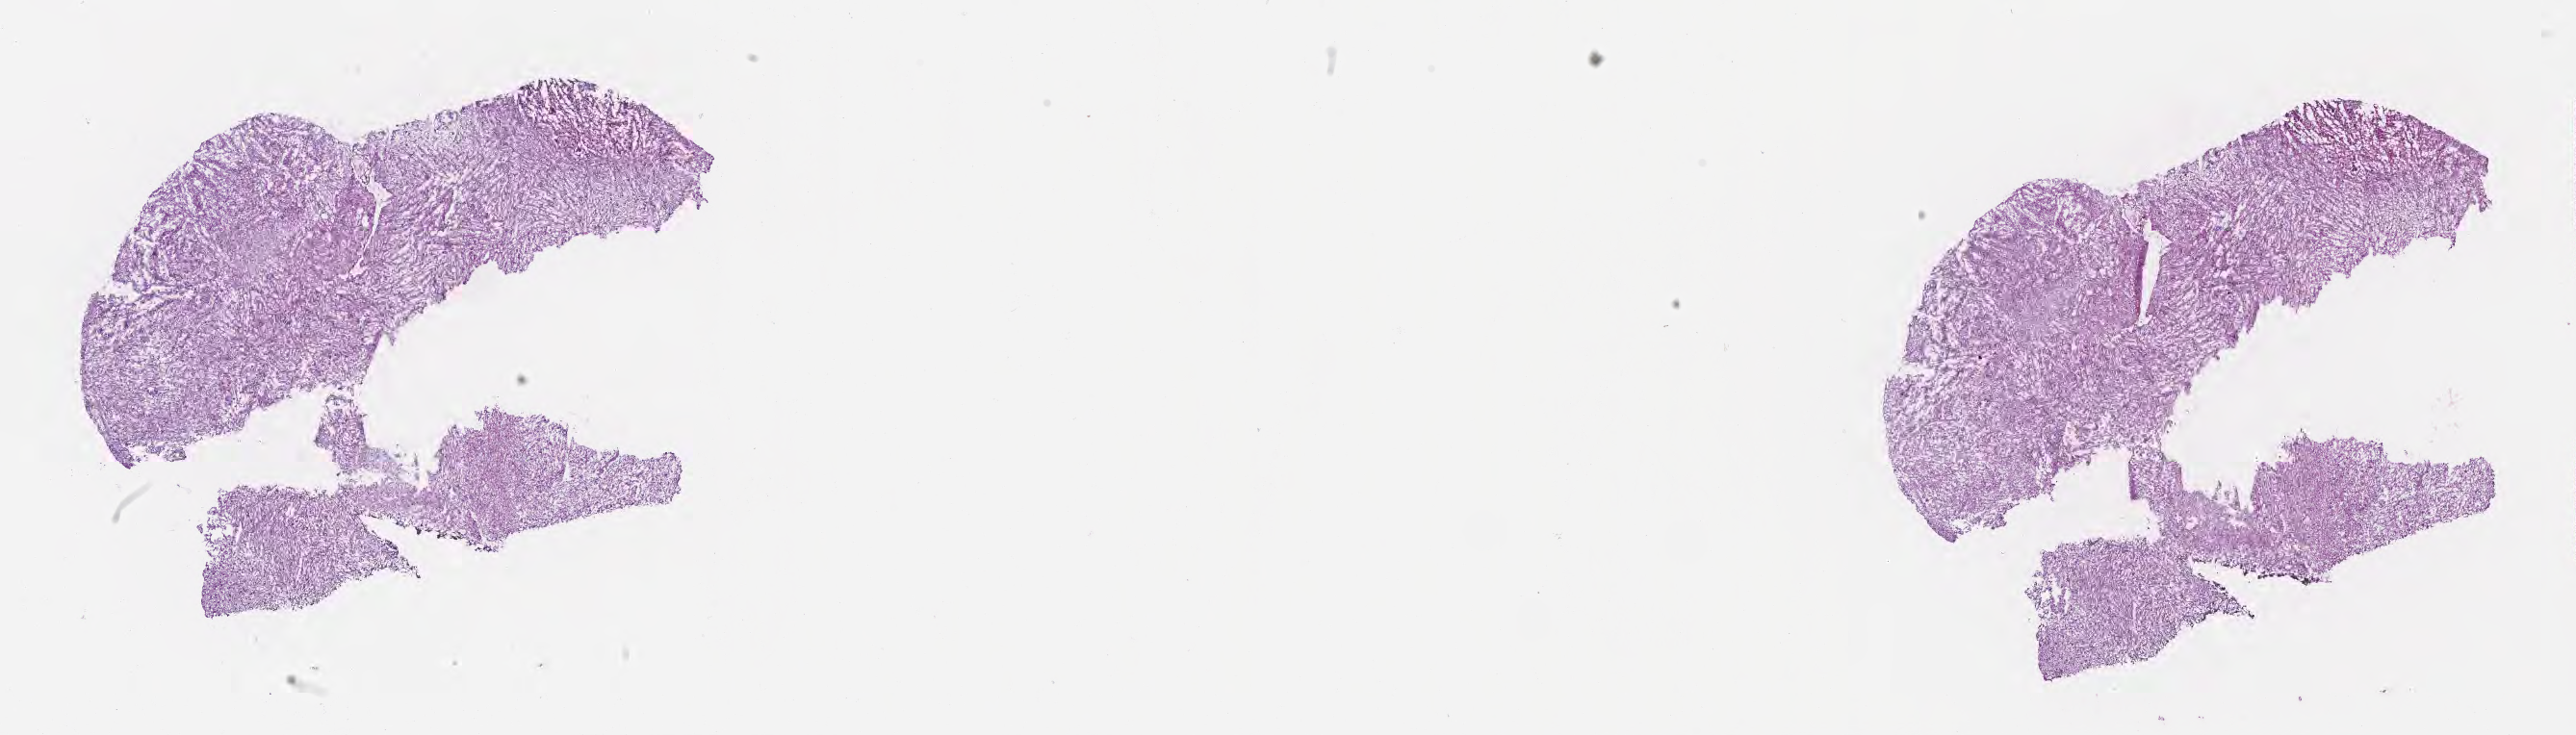
Digitized hematoxylin and eosin (H&E)-stained section — low-resolution overview of the scanned area, about 21.6 x 6.2 mm; frozen section; specimen: primary tumor; anatomic site: brain. Patient: female, age at initial diagnosis 58 years. Composition of this section per pathologist review: tumor cells 78%, tumor nuclei 87%, stromal cells 10%, necrosis 0%, normal cells 12%. Infiltration values recorded for this section: lymphocyte infiltration 0%, monocyte infiltration 0%, neutrophil infiltration 0%.
- histologic diagnosis: Glioblastoma, NOS